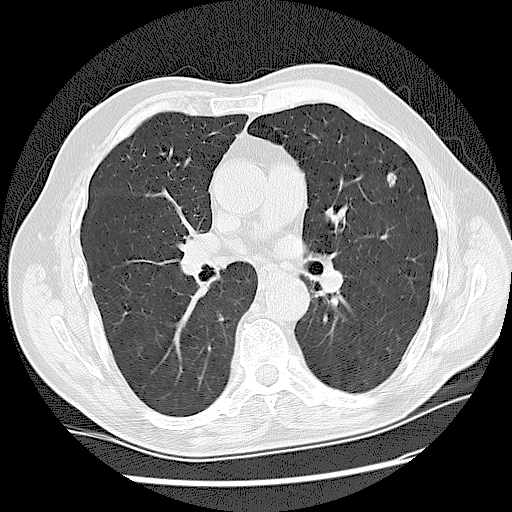
Low-dose screening chest CT, one axial slice. Slice 86 of 159 in the series (ordered by position). Reconstruction kernel LUNG. Lung window (W 1500 / L -600 HU). 2.5 mm slice thickness. 512 × 512 image matrix, field of view 360 × 360 mm.
Structures marked on this image (manually delineated by an expert):
- lesion 1 (tumor, upper lobe of left lung): bounding box <387,173,396,187> (left, top, right, bottom; pixels)